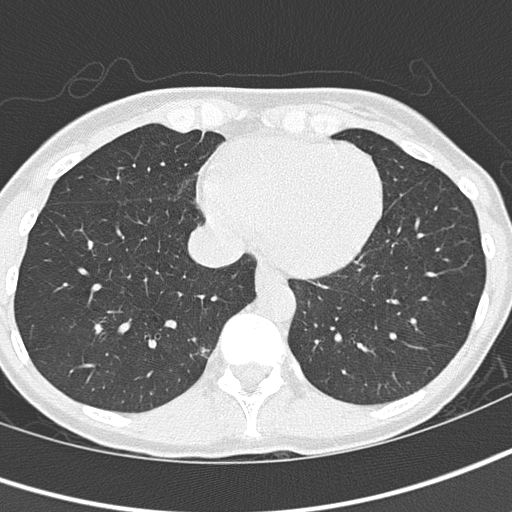
Low-dose screening chest CT, one axial slice. Position 44 of 145 along the scan axis. 120 kVp. Lung window (W 1500 / L -600 HU). 2 mm slice thickness. 512 × 512 image matrix, field of view 276 × 276 mm.
Outlined on this slice (outlined manually by an expert reader):
- lesion 1 (tumor, lower lobe of right lung): box from (x=202, y=348) to (x=209, y=356) px